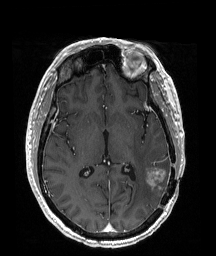
Brain MRI from a brain-tumour surgery series, one axial slice; slice 95 of 192 in the series (ordered by position); T1-weighted post-contrast; 1 mm slice thickness; 216 × 256 image matrix, field of view 211 × 250 mm. From the clinical record (not read from this slice): histopathology: Glioblastoma; WHO grade: 4; IDH mutation: no; tumour location: Left Temporoparietal.
Annotated regions visible in this slice (manually delineated by an expert):
- tumour: bounding box [x1, y1, x2, y2] px = [144, 166, 170, 187]